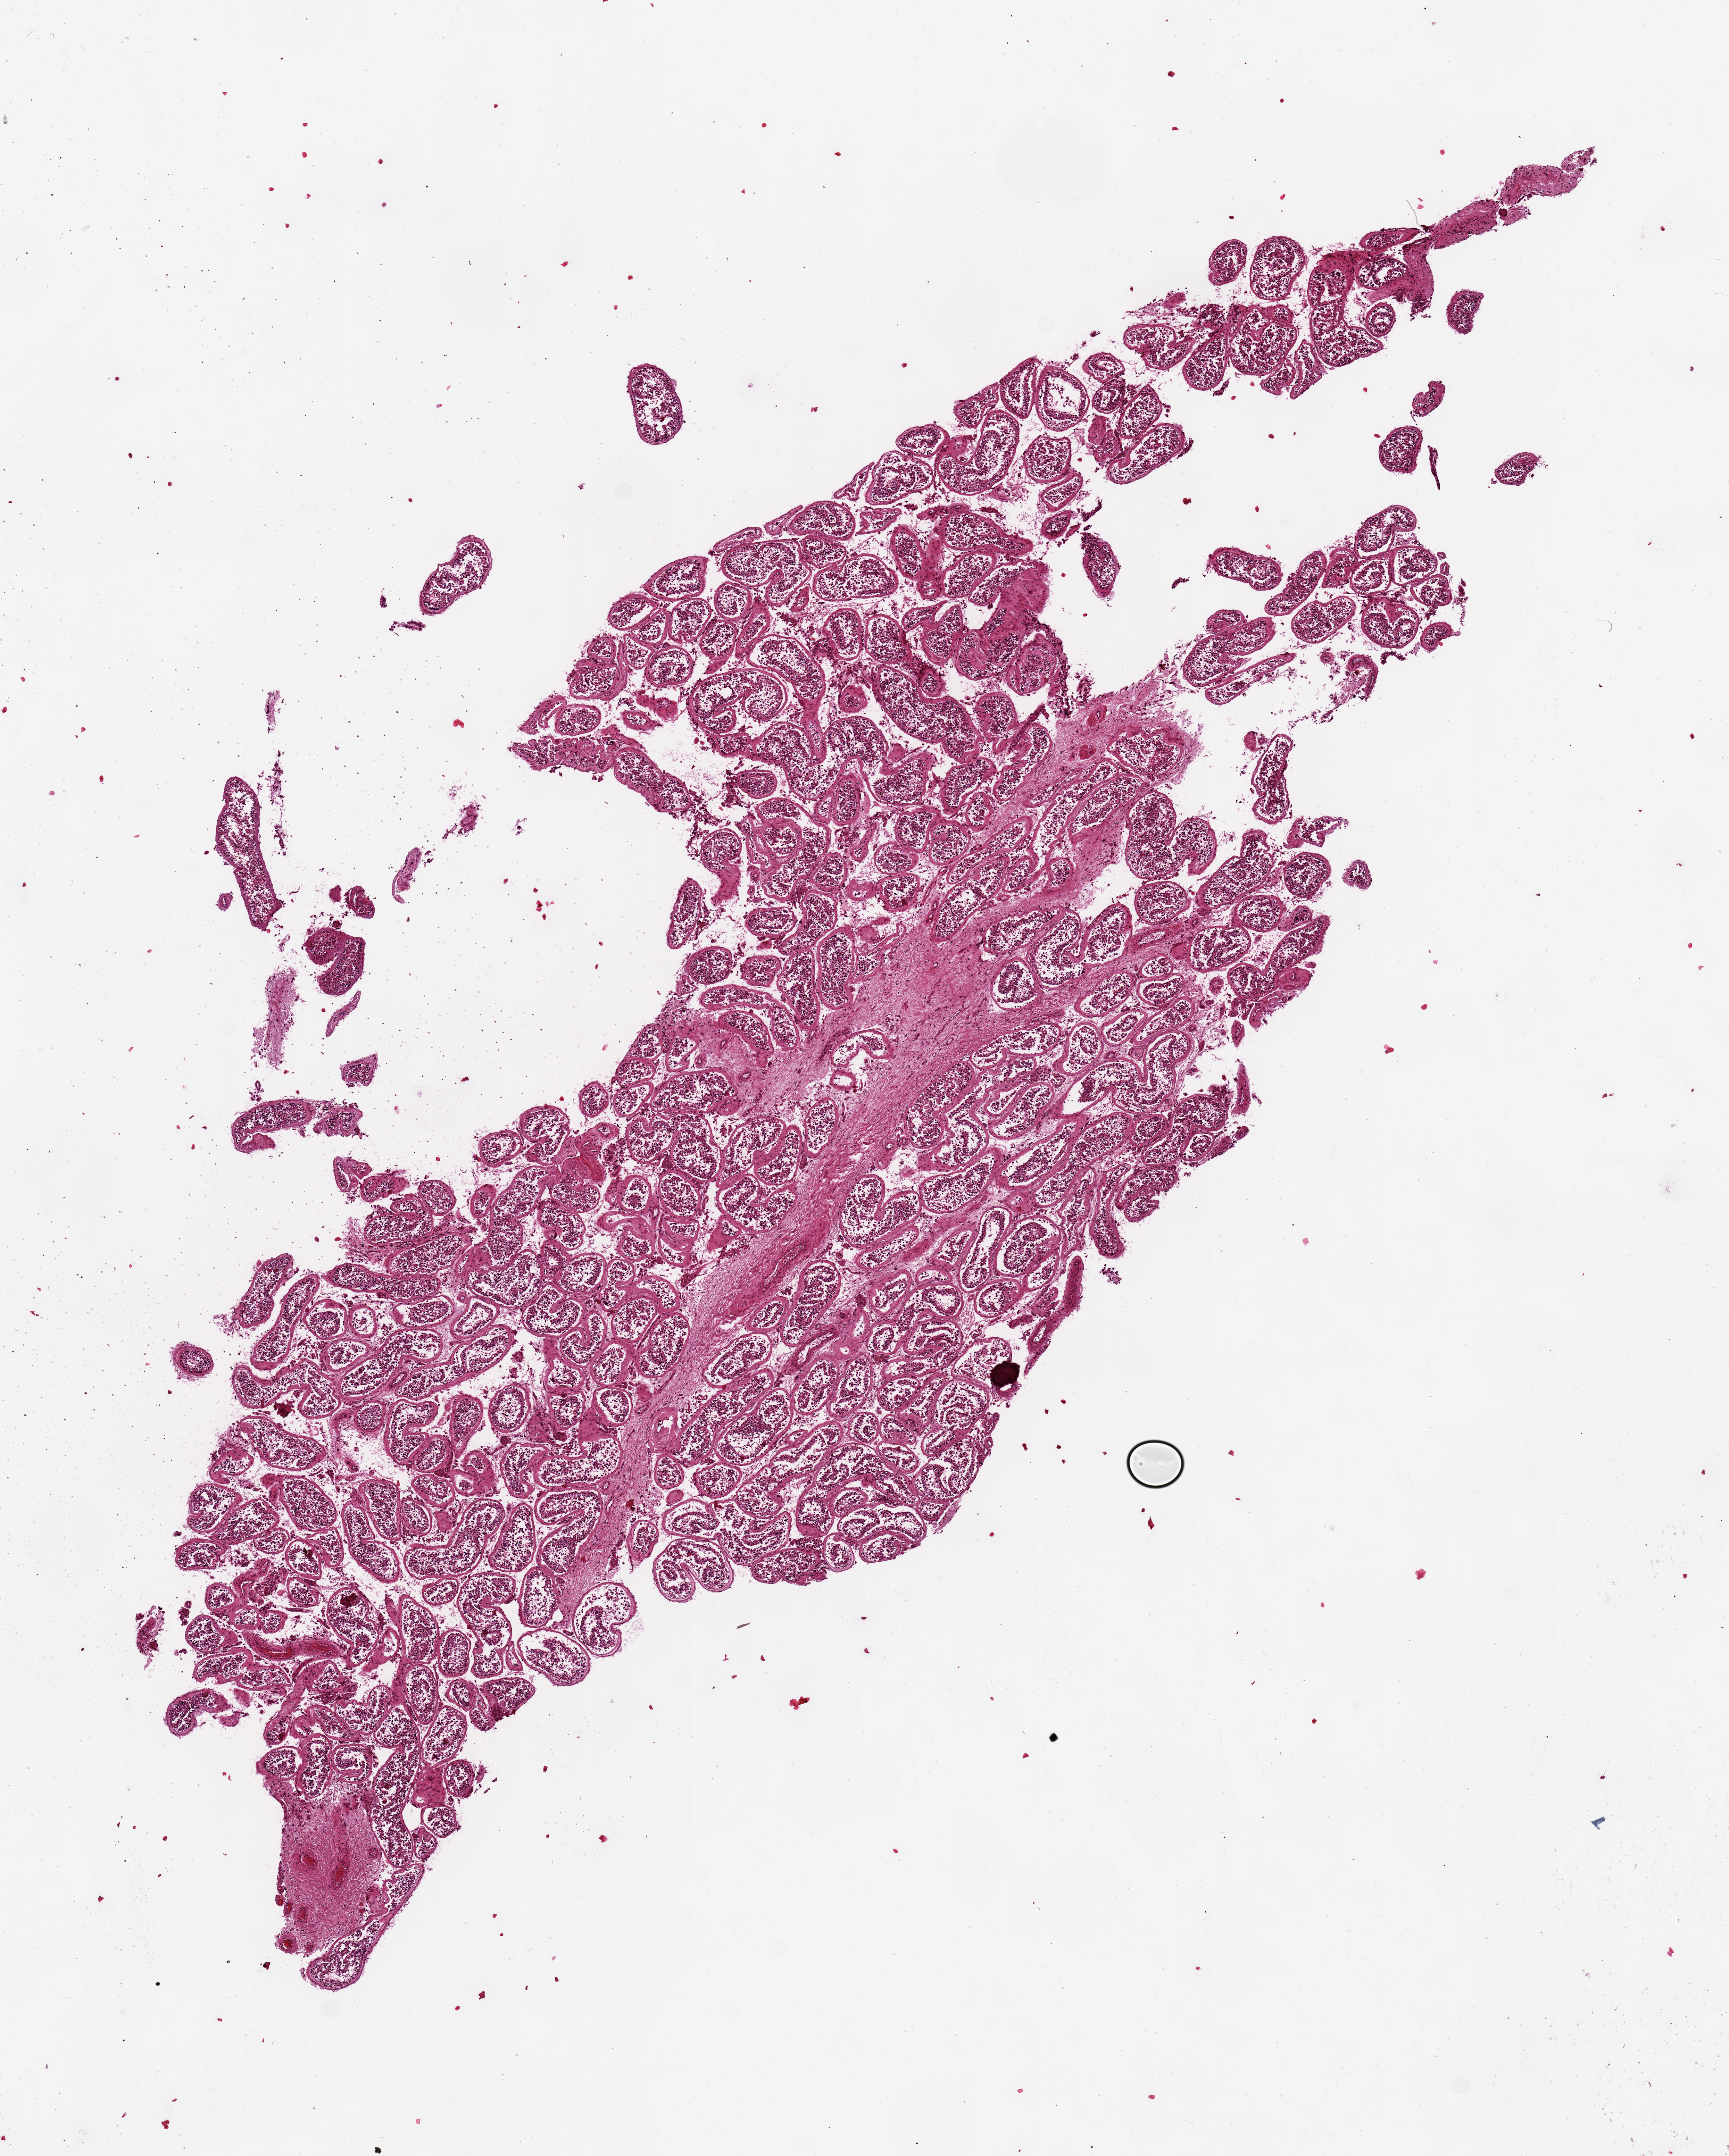
Haematoxylin and eosin whole-slide image, brightfield — low-resolution overview of the scanned area, about 9.8 x 12.3 mm (slide scanned at 20x). PAXgene-fixed, paraffin-embedded tissue. Section of testis (target tissue). Tissue donor sample. Donor: male.
• review note (as recorded): 12x5 mm